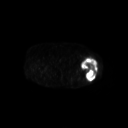
FDG PET of an extremity soft-tissue mass (from a PET/CT study), one axial slice; position 238 of 267 along the scan axis; 128 × 128 image matrix, field of view 700 × 700 mm. Patient: female, 62 years. From the clinical record (not read from this slice): histological type: undifferentiated – high grade; grade: high; site of the primary tumour: left thigh.
Annotated regions visible in this slice (expert contour drawn on MRI and transferred to this co-registered scan by the dataset authors):
- gross tumour volume including surrounding oedema: bounding box (x1, y1, x2, y2) in pixels: (81, 58, 98, 81)
- gross tumour volume (mass): (81, 58, 98, 81)